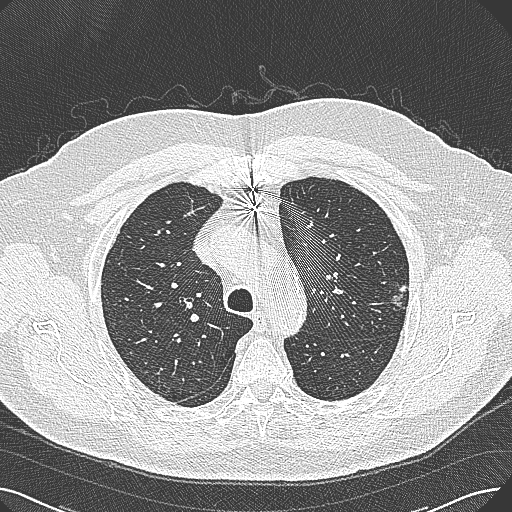
Low-dose screening chest CT, axial slice; baseline annual screen; lung window (W 1500 / L -600 HU). Male, age 74 years at enrolment. Former smoker at enrolment.
Expert reader's lesion annotation, bounding box (x1, y1, x2, y2) in pixels: (377, 273, 422, 316). Reader record for this screening exam (exam-level; its link to the box is not recorded): non-calcified nodule or mass ≥4 mm, left upper lobe, 15 × 10 mm, poorly defined margins, soft tissue attenuation.